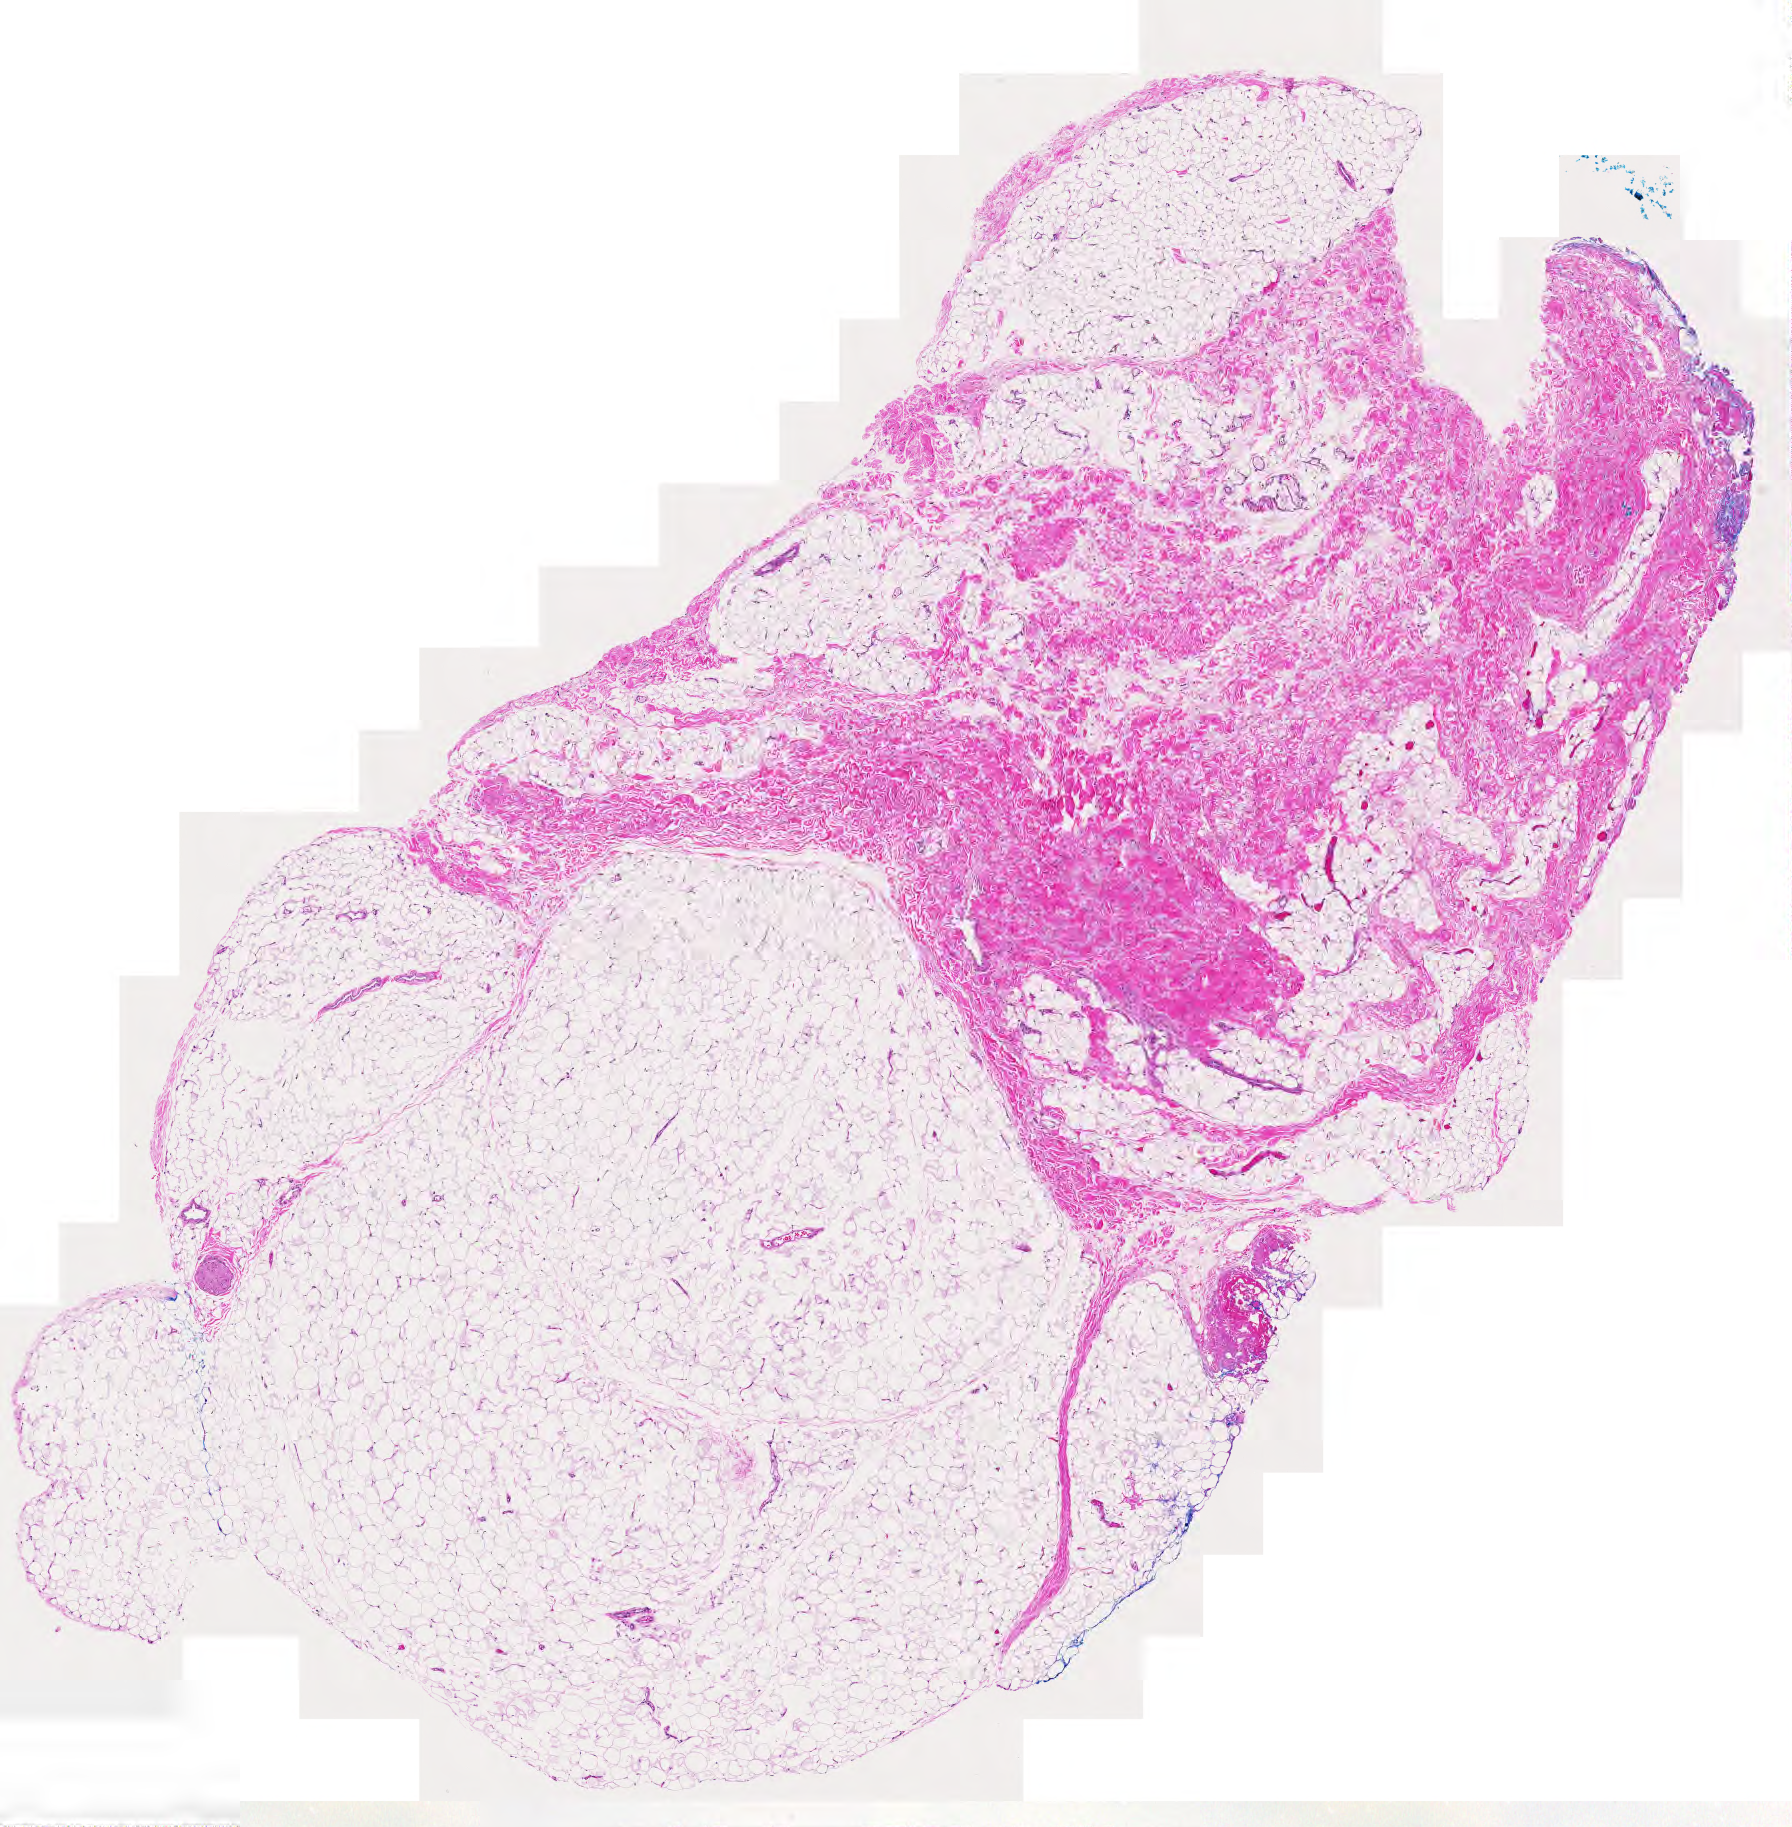
H&E whole-slide image, low-resolution overview of the scanned area, about 9.2 x 9.4 mm (slide scanned at 20x). Normal (non-tumour) tissue sample. 41-year-old female patient.
This section: normal (non-tumour) tissue from the same patient. Patient diagnosis (cohort enrolment): sarcoma (site not recorded at cohort level).